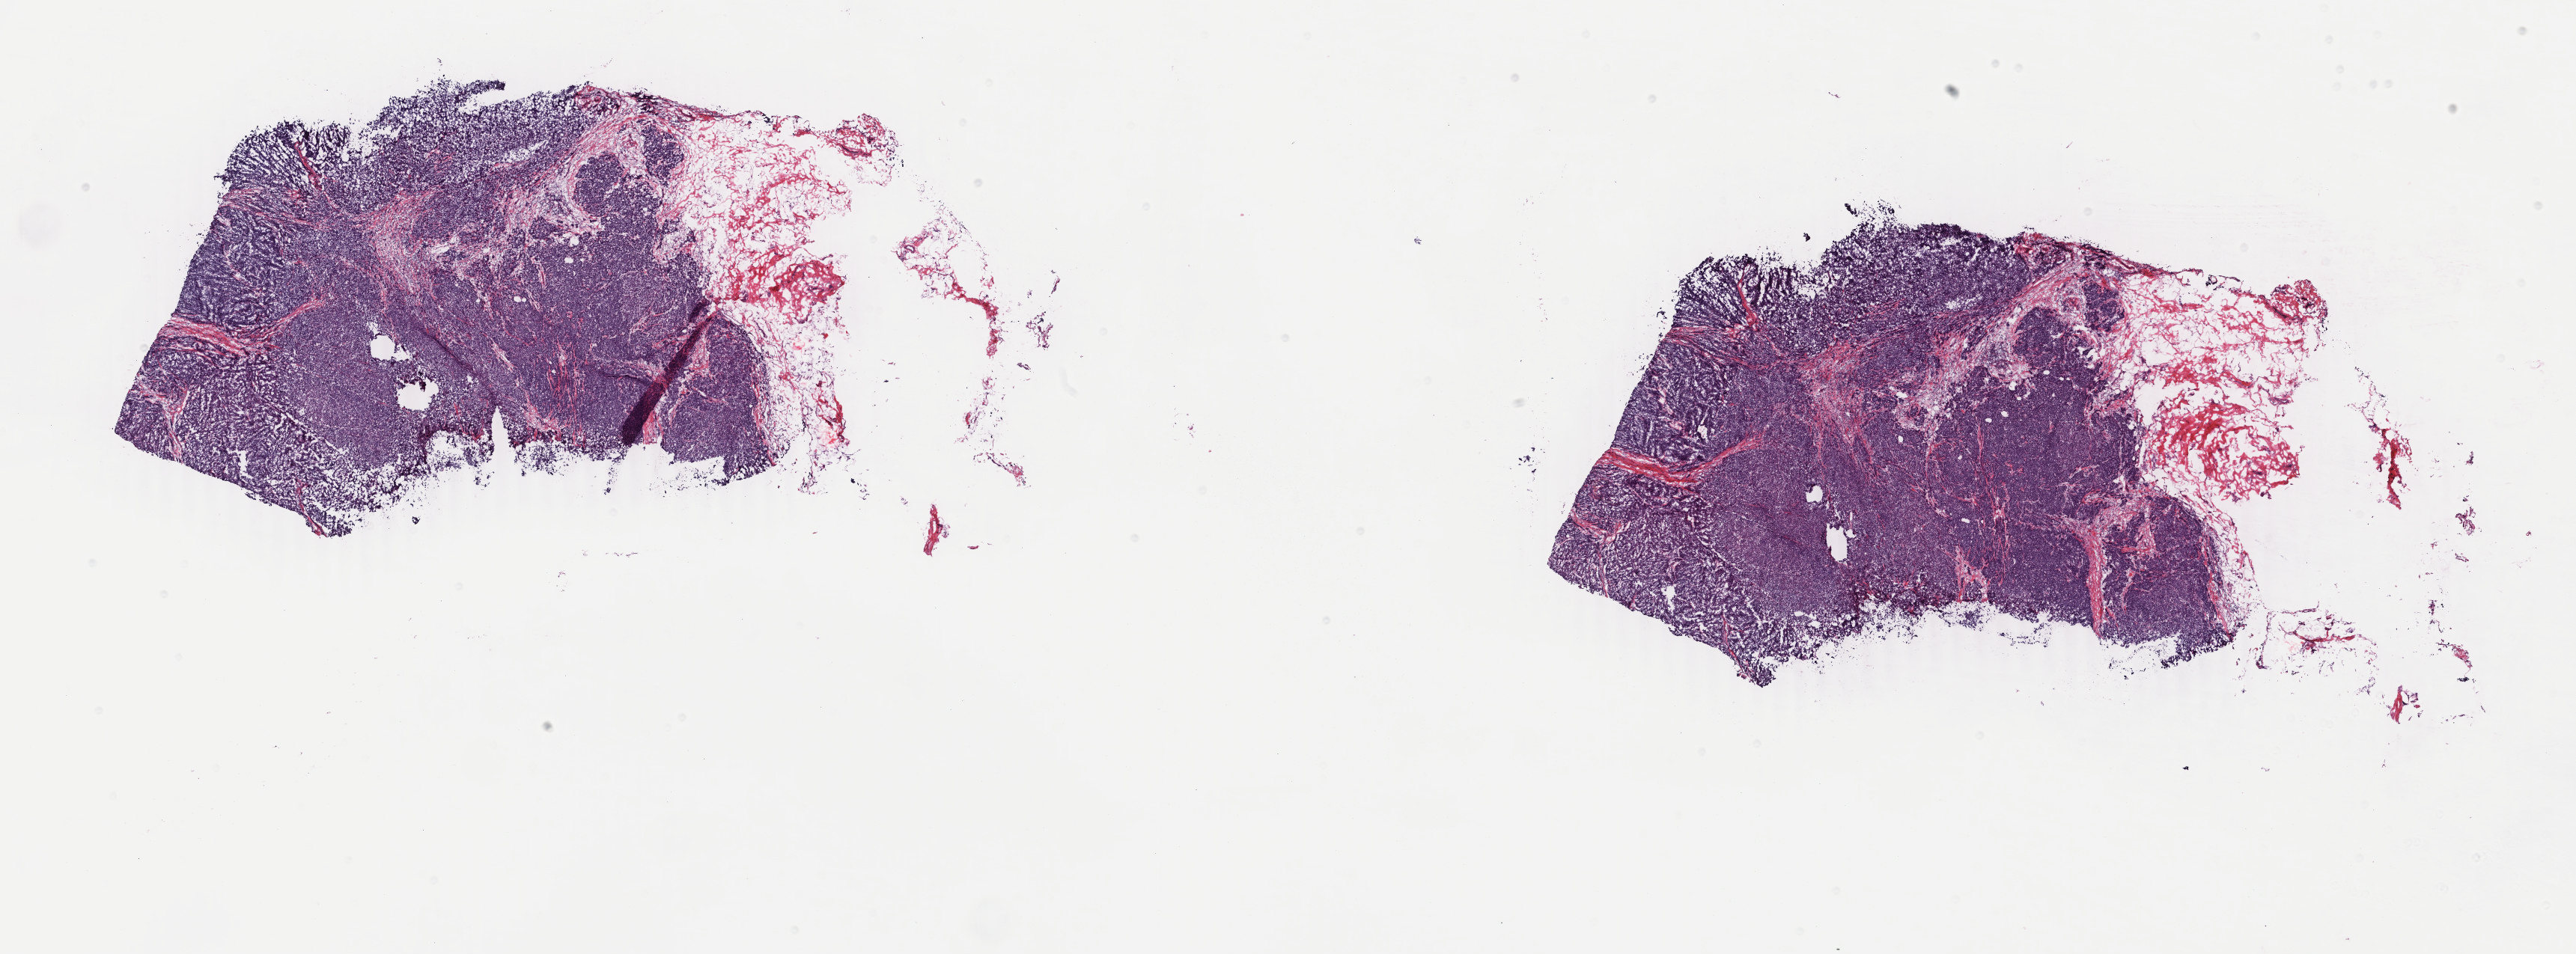
Digitized H&E tissue section (whole slide), low-resolution overview of the scanned area, about 27.4 x 10.1 mm (acquisition: 40x scan). Frozen section. Breast, primary tumour sample. Female, age 58 years at initial diagnosis. Composition of this section per pathologist review: tumour cells 79%, tumour nuclei 90%, normal cells 15%, stromal cells 5%, necrosis 1%. Inflammatory infiltration, as recorded: lymphocyte infiltration 5%, monocyte infiltration 0%, neutrophil infiltration 0%.
- diagnosis: Infiltrating duct carcinoma, NOS
- TNM: T2 N2a M0
- lymph nodes positive (case pathology): 5 of 15 examined
- AJCC pathologic stage: IIIA (6th edition)